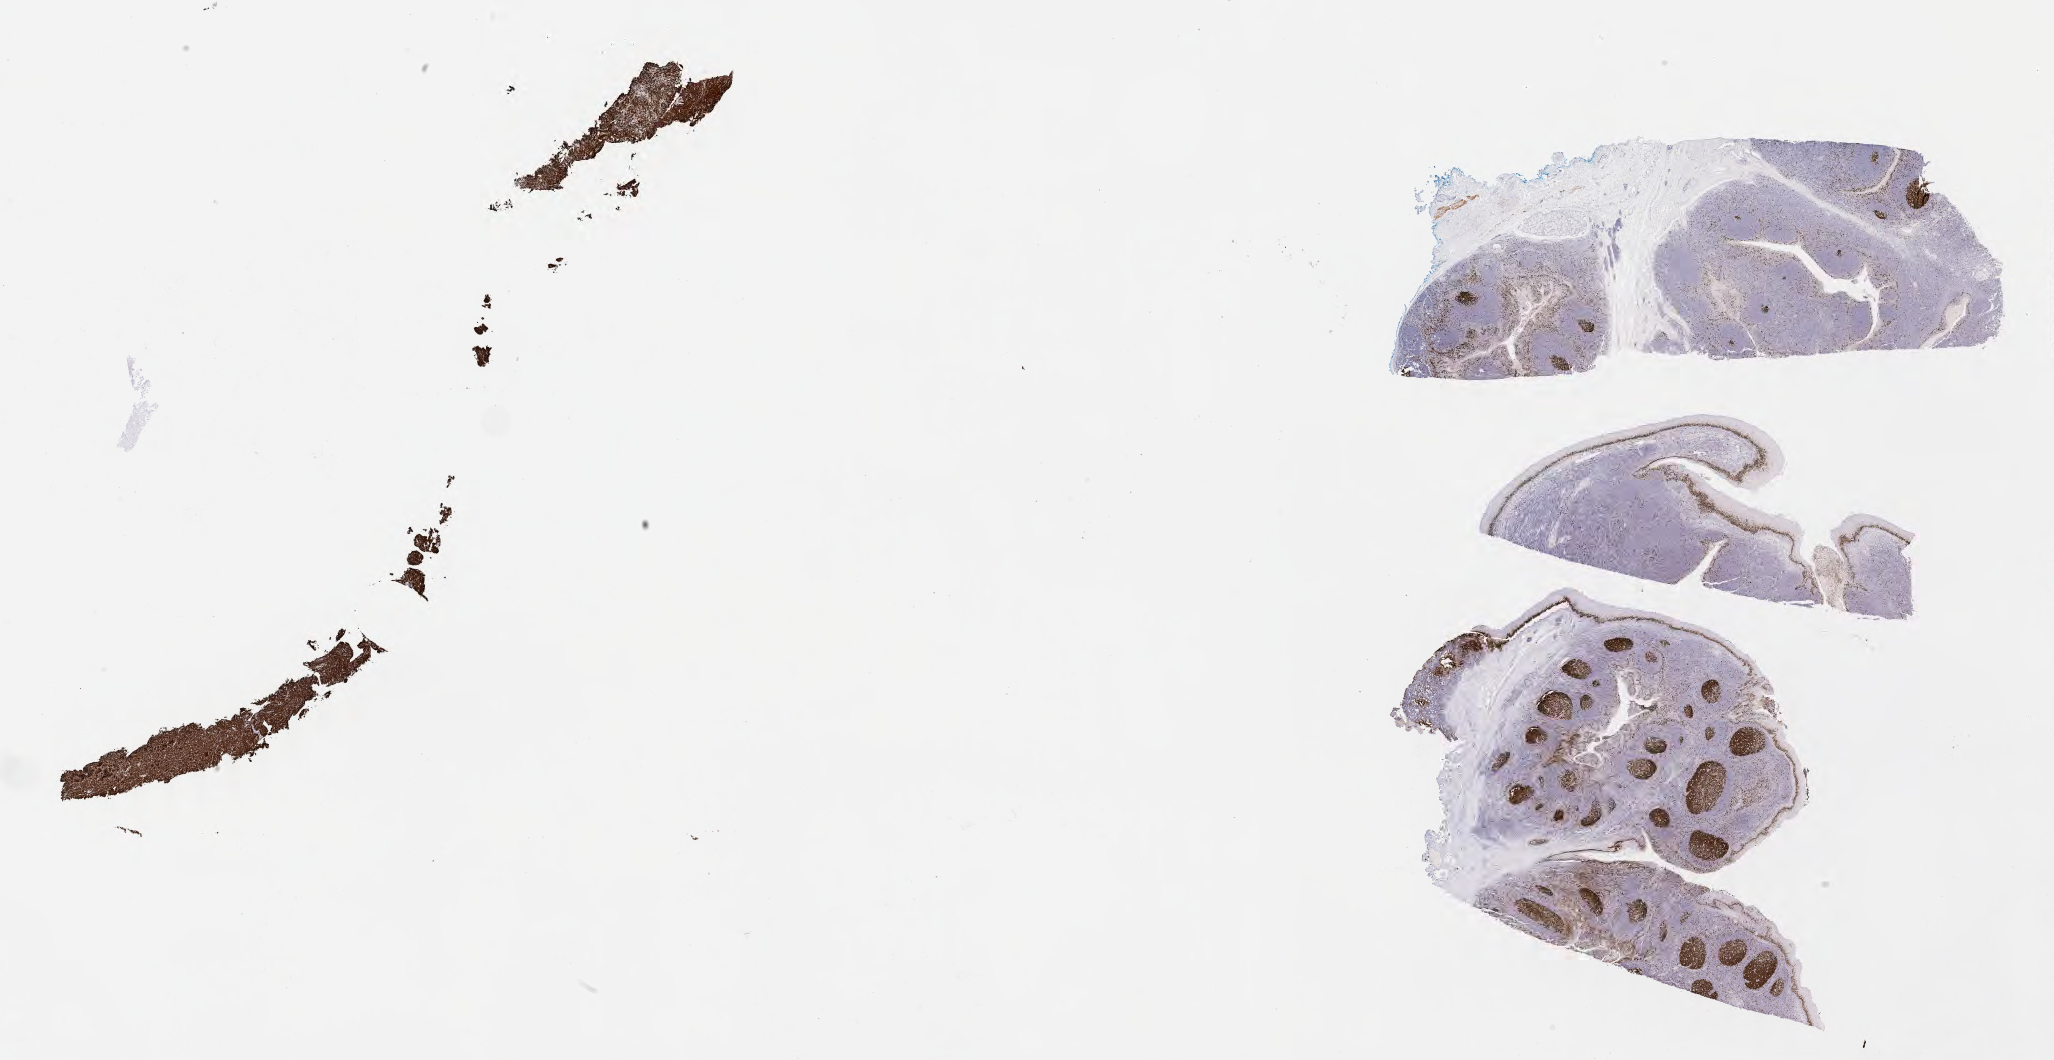
Whole-slide image, immunohistochemical stain for Ki-67, low-resolution overview of the scanned area, about 33.2 x 17.1 mm, specimen: tumor tissue, anatomic site: cranium. Female, age 7 years at initial diagnosis.
- diagnosis: Burkitt lymphoma, NOS